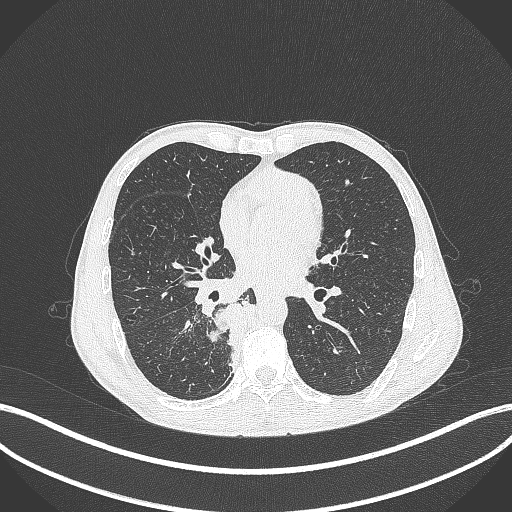
Chest CT, one axial slice. Position 179 of 371 along the scan axis. Reconstruction kernel B70f. 120 kVp. Lung window (W 1500 / L -600 HU). 512 × 512 image matrix, field of view 400 × 400 mm. Male patient, age 58 years. From the clinical record (not read from this slice): clinical TNM (as recorded): T3 N1 M1.
Outlined on this slice (bounding box drawn by a radiologist):
- lung tumour (recorded histology: squamous cell carcinoma): box from (x=201, y=300) to (x=264, y=370) px